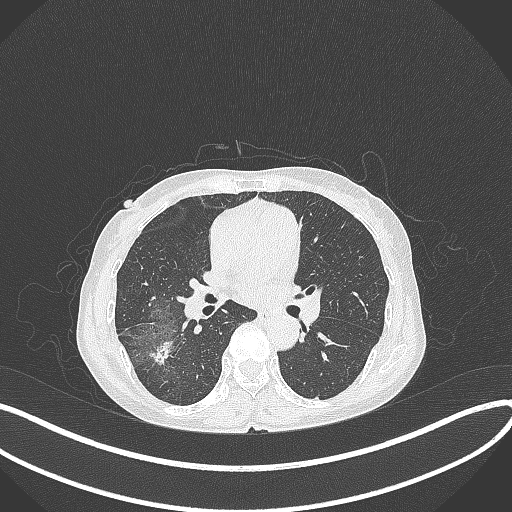
Chest CT, one axial slice. Slice 210 of 371 in the series (ordered by position). Lung window (W 1500 / L -600 HU). 1 mm slice thickness. 512 × 512 image matrix. Patient: female, 69 years. Case-level facts recorded for this patient, not image findings: clinical TNM (as recorded): T1b N0 M0; histopathological grade: G2-3.
Outlined on this slice (bounding box drawn by a radiologist):
- lung tumour (recorded histology: adenocarcinoma): bounding box <147,336,176,368> (left, top, right, bottom; pixels)